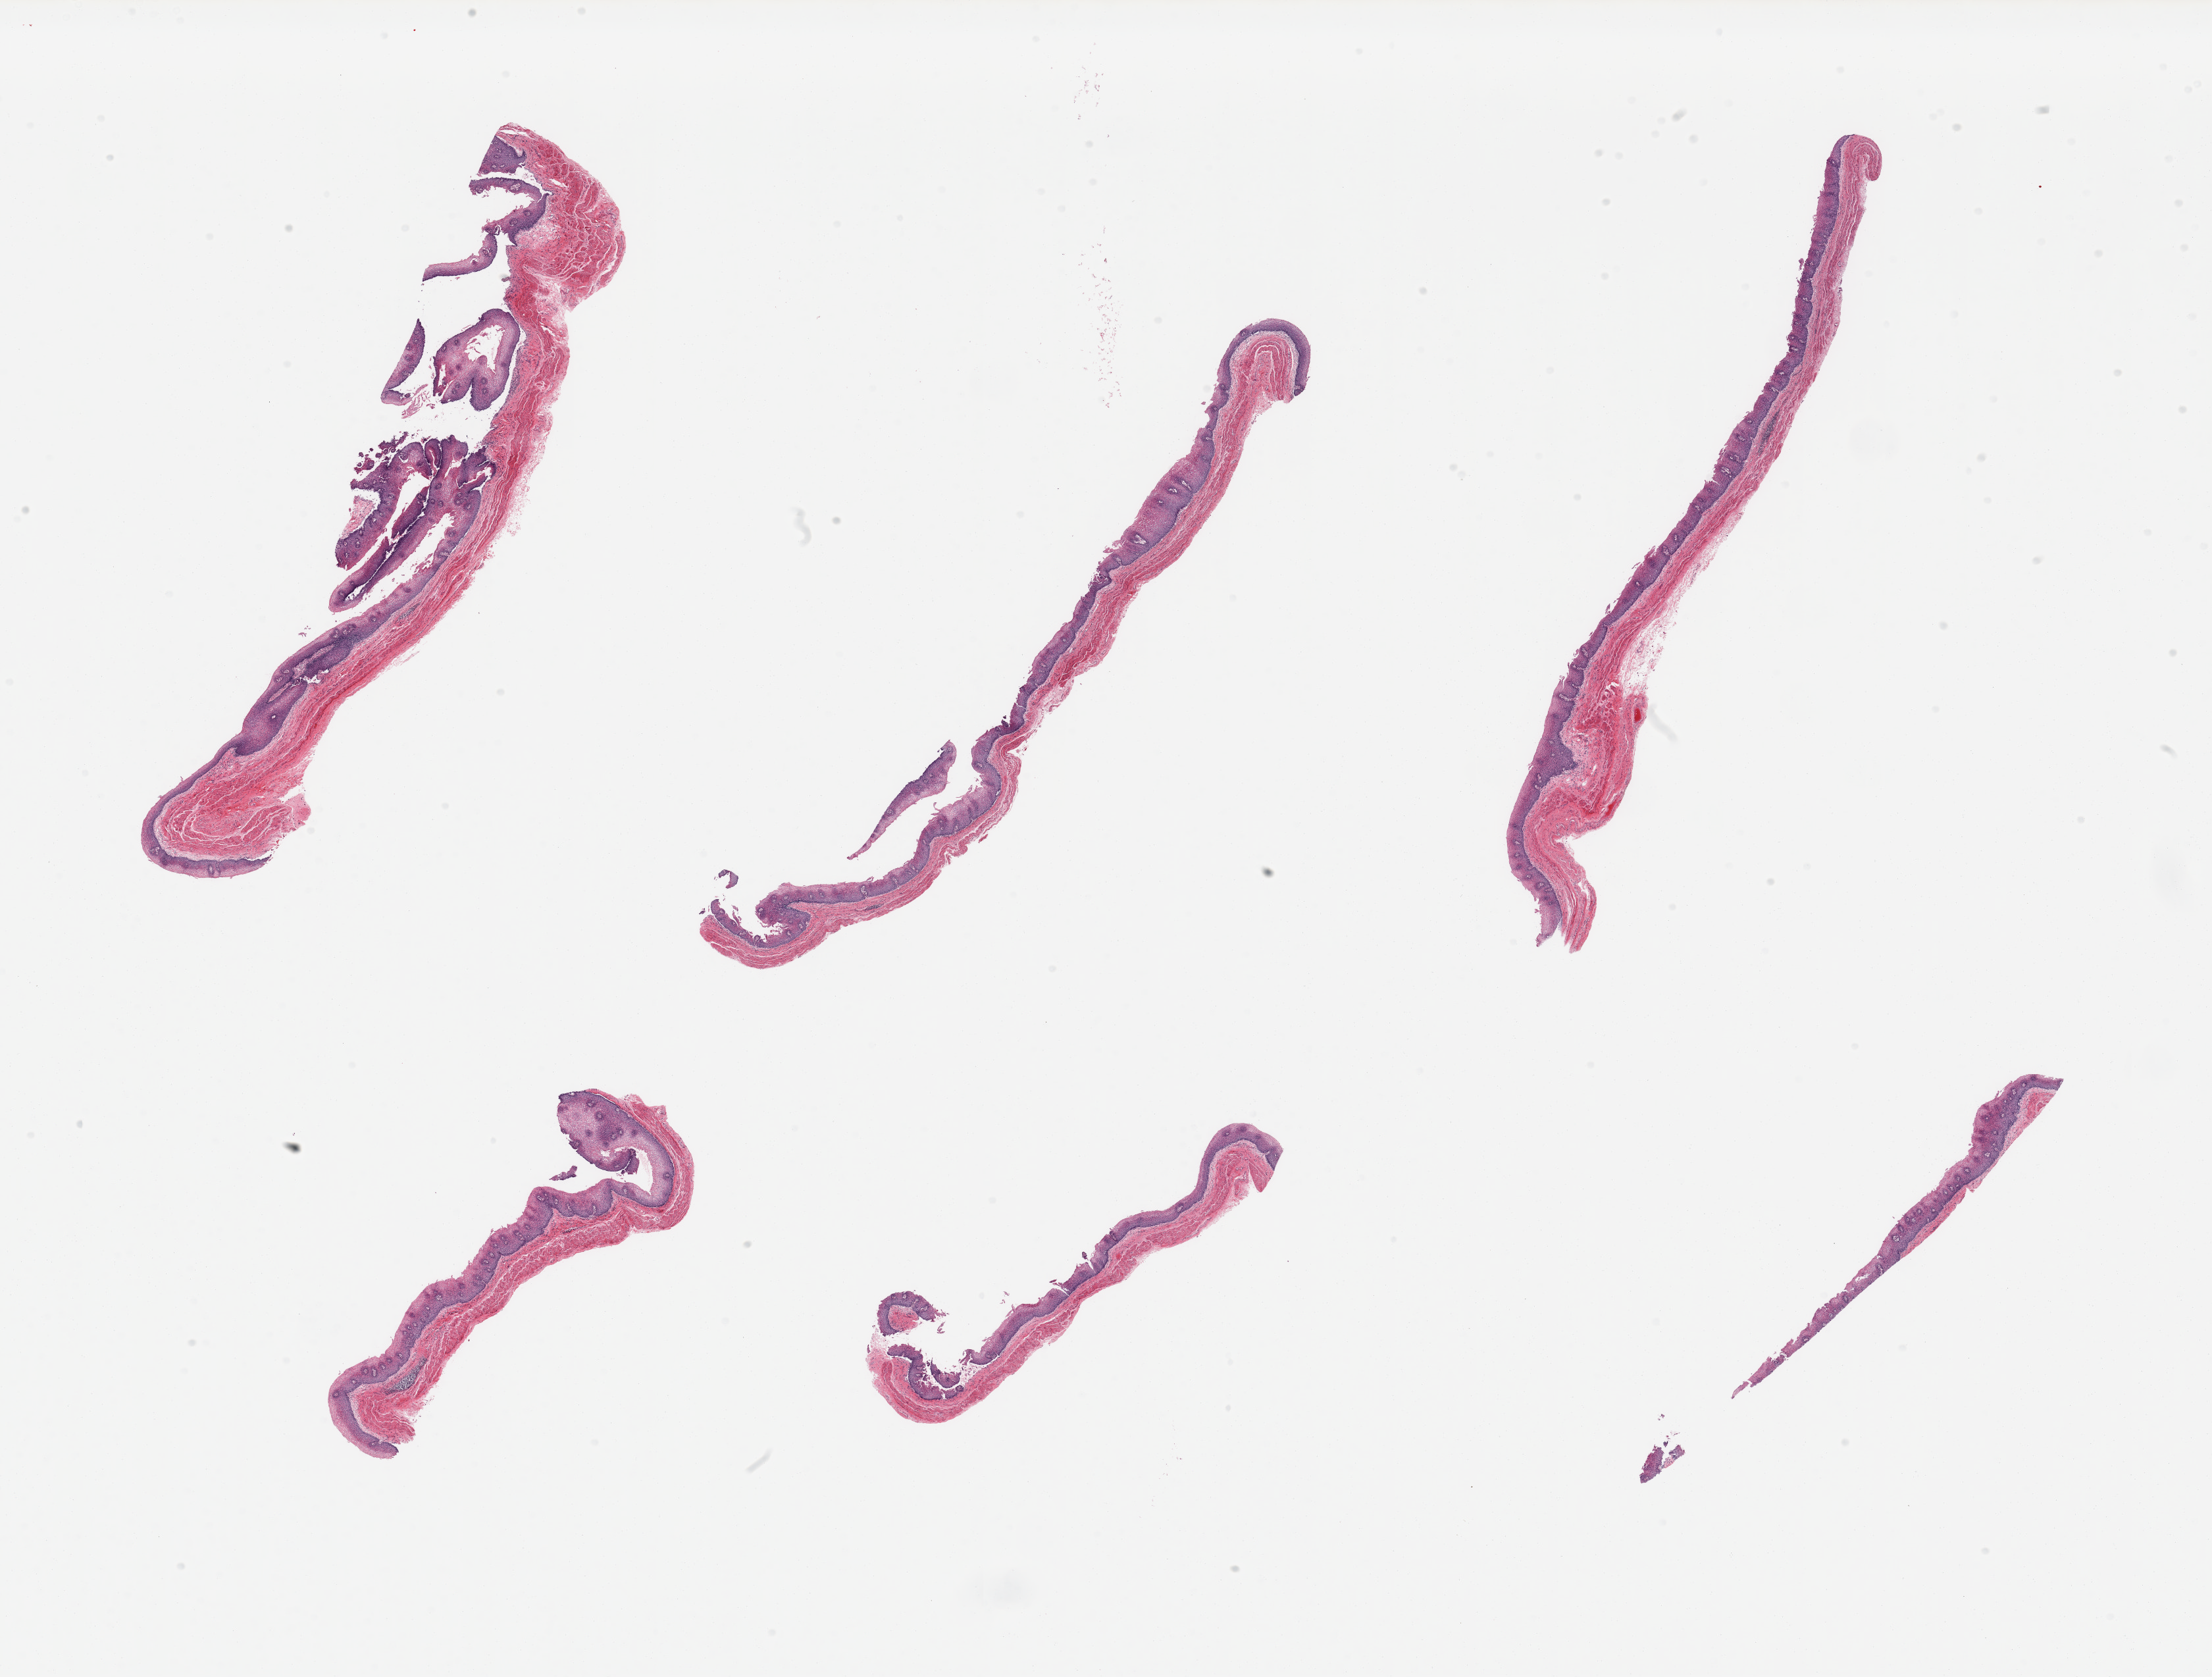
Whole-slide image, hematoxylin and eosin (H&E) stain, a low-resolution overview of the entire scanned area, about 26.6 x 20.2 mm (slide scanned at 20x); PAXgene-fixed paraffin-embedded (PFPE) section; section of esophageal mucous membrane (target tissue); donor tissue sample. Male donor.
Review note (as recorded): 6 pieces; squamous epithelium ~0.3mm thick; well dissected mucosa.